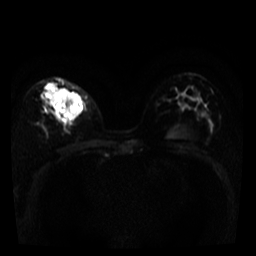
Breast MRI, one axial slice; slice 23 of 39 in the series (ordered by position); diffusion-weighted series; image 2 of 4 stored at this slice position (different b-values; order by instance number); 3 T; 5 mm slice thickness; 256 × 256 image matrix, field of view 280 × 280 mm. Female patient.
Outlined on this slice (expert manual segmentation):
- tumour on diffusion-weighted imaging: bounding box (x1, y1, x2, y2) in pixels: (46, 83, 85, 116)